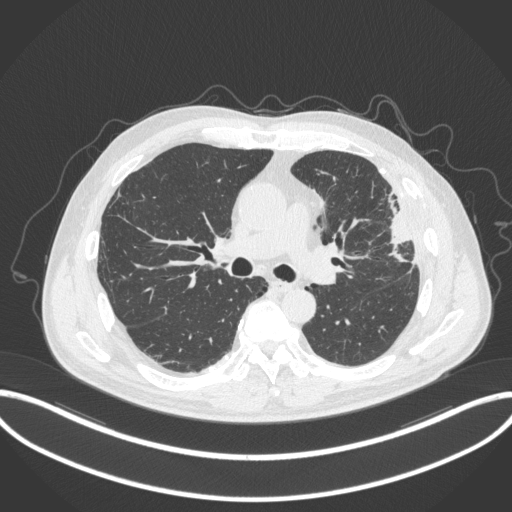
Chest CT, one axial slice. Slice 204 of 382 in the series (ordered by position). Reconstruction kernel B31f. 120 kVp. Lung window (W 1500 / L -600 HU). 512 × 512 image matrix, field of view 415 × 415 mm. Patient: male, 64 years. From the clinical record (not read from this slice): clinical TNM (as recorded): T4 N1 M0; histopathological grade: G3.
Structures marked on this image (bounding box drawn by a radiologist):
- lung tumour (recorded histology: adenocarcinoma): bounding box [x1, y1, x2, y2] px = [383, 193, 416, 261]